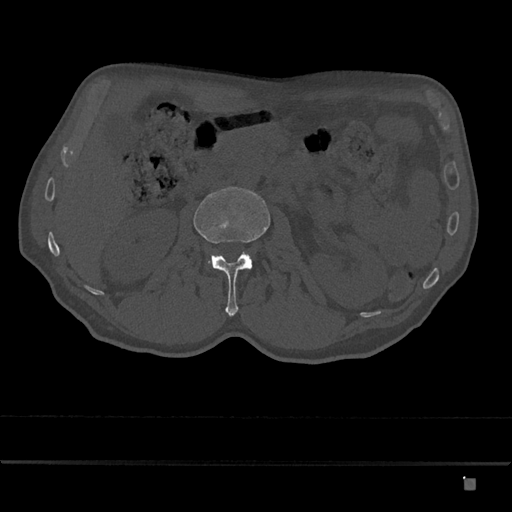
CT including the spine, one axial slice; position 465 of 797 along the scan axis; reconstruction kernel Br40s/3; bone window (W 1800 / L 400 HU); 512 × 512 image matrix, field of view 390 × 390 mm. Male patient, age 72 years. From the clinical record (not read from this slice): primary cancer: prostate.
Structures marked on this image (semi-automatic segmentation, software-assisted and operator-edited):
- L2 vertebra: bounding box [x1, y1, x2, y2] px = [194, 187, 270, 316]